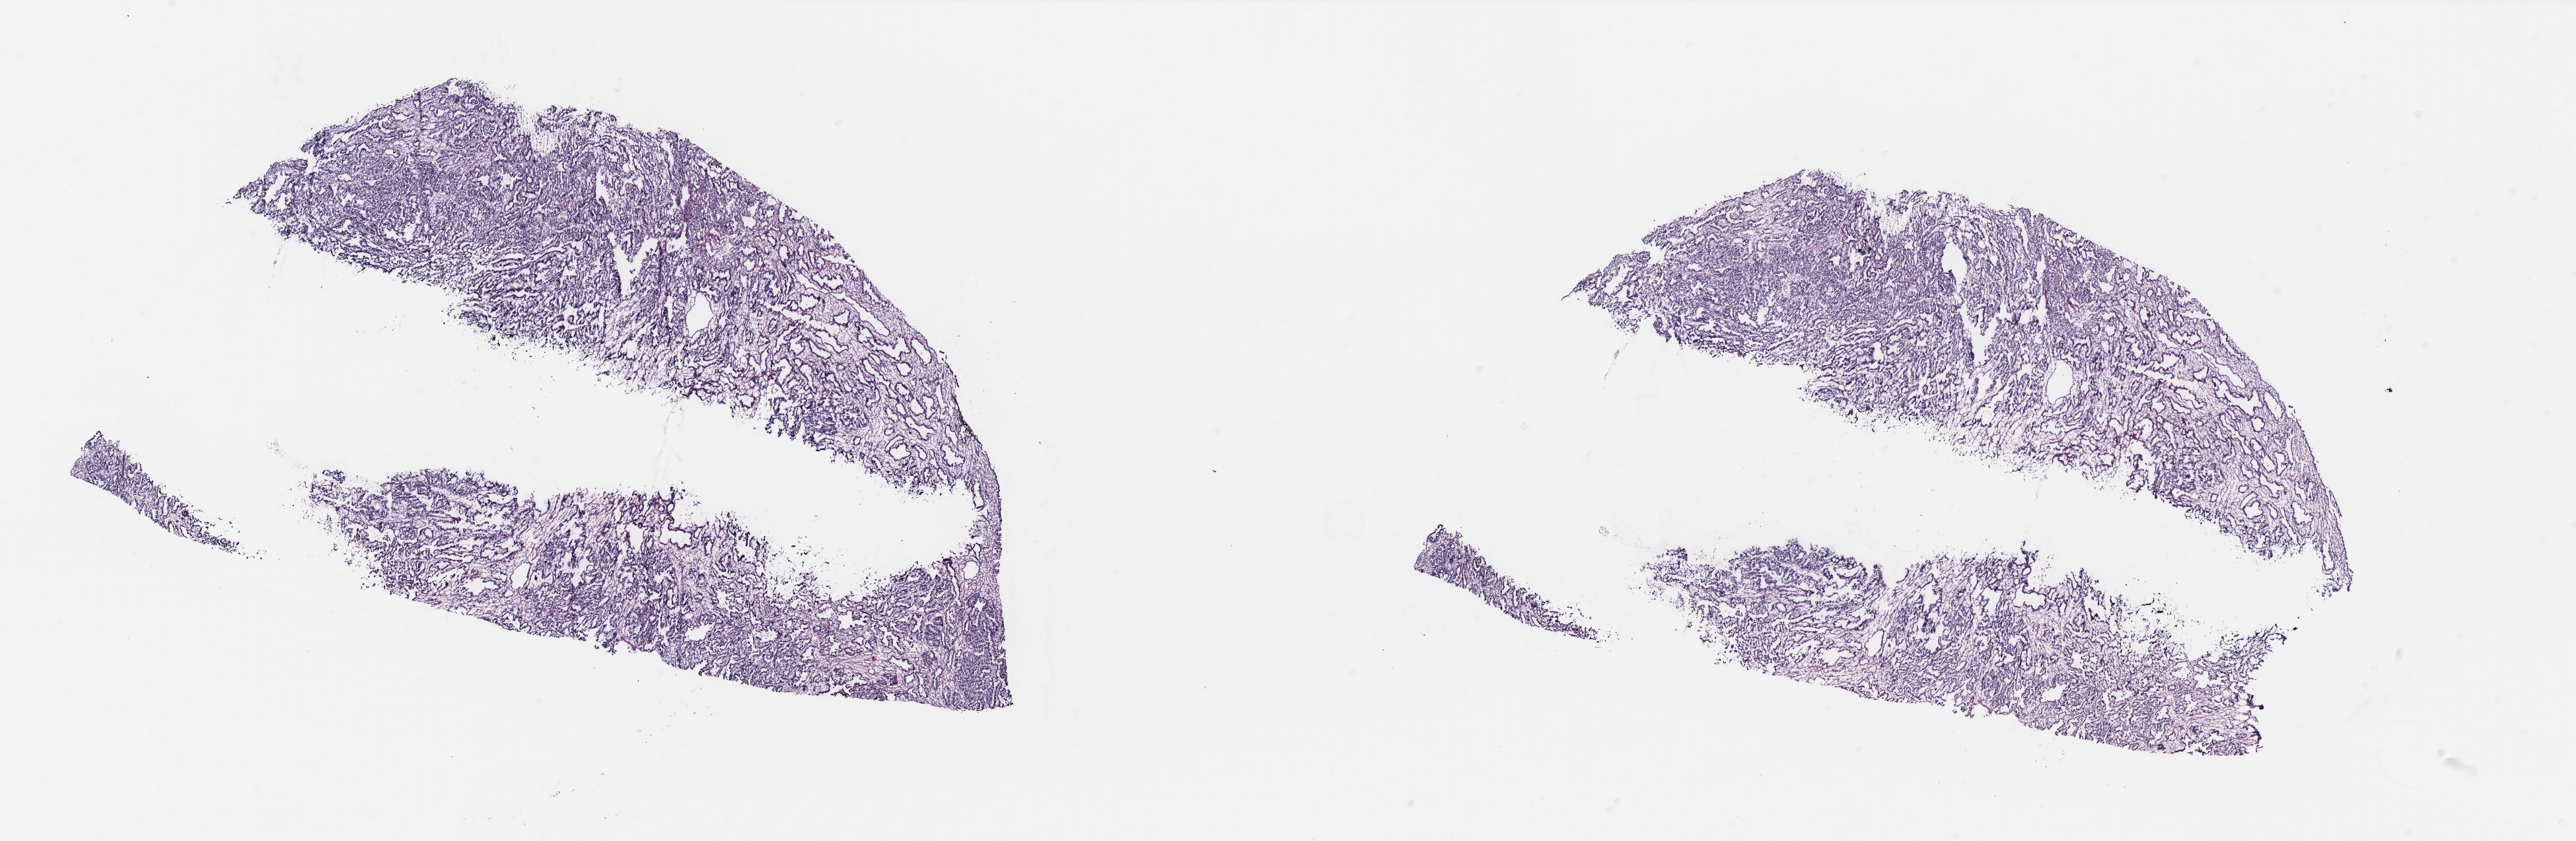
Digitized H&E tissue section (whole slide) — a low-resolution overview of the entire scanned area, about 31.3 x 10.2 mm; frozen section from the bottom of the tissue portion; primary tumour sample from the uterus. Patient: female, age at initial diagnosis 60 years. Histologic grade: G3 (poorly differentiated). Slide review estimates, as recorded: tumour cells 70%, tumour nuclei 60%, normal cells 30%, stromal cells 0%, necrosis 0%. Infiltration values recorded for this section: lymphocyte infiltration 0%, monocyte infiltration 0%, neutrophil infiltration 0%.
• lymph nodes positive (case pathology): 0 of 17 examined
• histologic diagnosis: Serous cystadenocarcinoma, NOS (endometrium)
• FIGO stage: IA